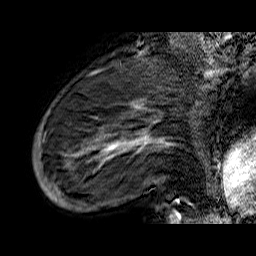
Breast MRI (dynamic contrast-enhanced), one sagittal slice; position 14 of 60 along the scan axis; dynamic contrast-enhanced series, time point 2 of 6 at this slice position (early post-contrast); 1.5 T; TE 6.5 ms, TR 32.9 ms; 4 mm slice thickness; 256 × 256 image matrix, field of view 200 × 200 mm. Female patient. From the clinical record (not read from this slice): setting: breast cancer imaged before/during neoadjuvant chemotherapy; receptor status: HR-positive, HER2-negative.
Annotated regions visible in this slice (semi-automatically segmented with operator editing):
- analysis volume of interest (the breast-tissue region the enhancement analysis was run in; not a lesion): bounding box <33,74,176,210> (left, top, right, bottom; pixels)
- tumour enhancement mask (voxels above the 100 % enhancement threshold inside the analysis volume of interest): <38,103,176,203>